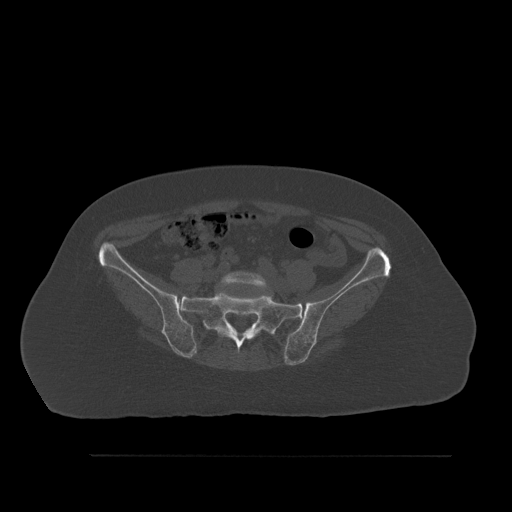
CT including the spine, one axial slice; slice 175 of 527 in the series (ordered by position); bone window (W 1800 / L 400 HU); 512 × 512 image matrix, field of view 470 × 470 mm. Patient: female, 73 years. From the clinical record (not read from this slice): primary cancer: breast.
Outlined on this slice (semi-automatic segmentation, software-assisted and operator-edited):
- L5 vertebra: bounding box (x1, y1, x2, y2) in pixels: (220, 271, 271, 329)